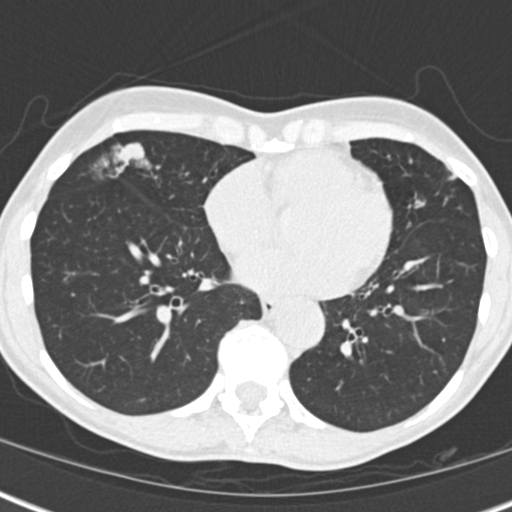
Low-dose screening chest CT, one axial slice; slice 67 of 173 in the series (ordered by position); reconstruction kernel B30f; 120 kVp; lung window (W 1500 / L -600 HU); 2 mm slice thickness; 512 × 512 image matrix, field of view 290 × 290 mm.
Structures marked on this image (expert manual segmentation):
- lesion 1 (tumor, middle lobe of right lung): bounding box (x1, y1, x2, y2) in pixels: (117, 144, 143, 164)